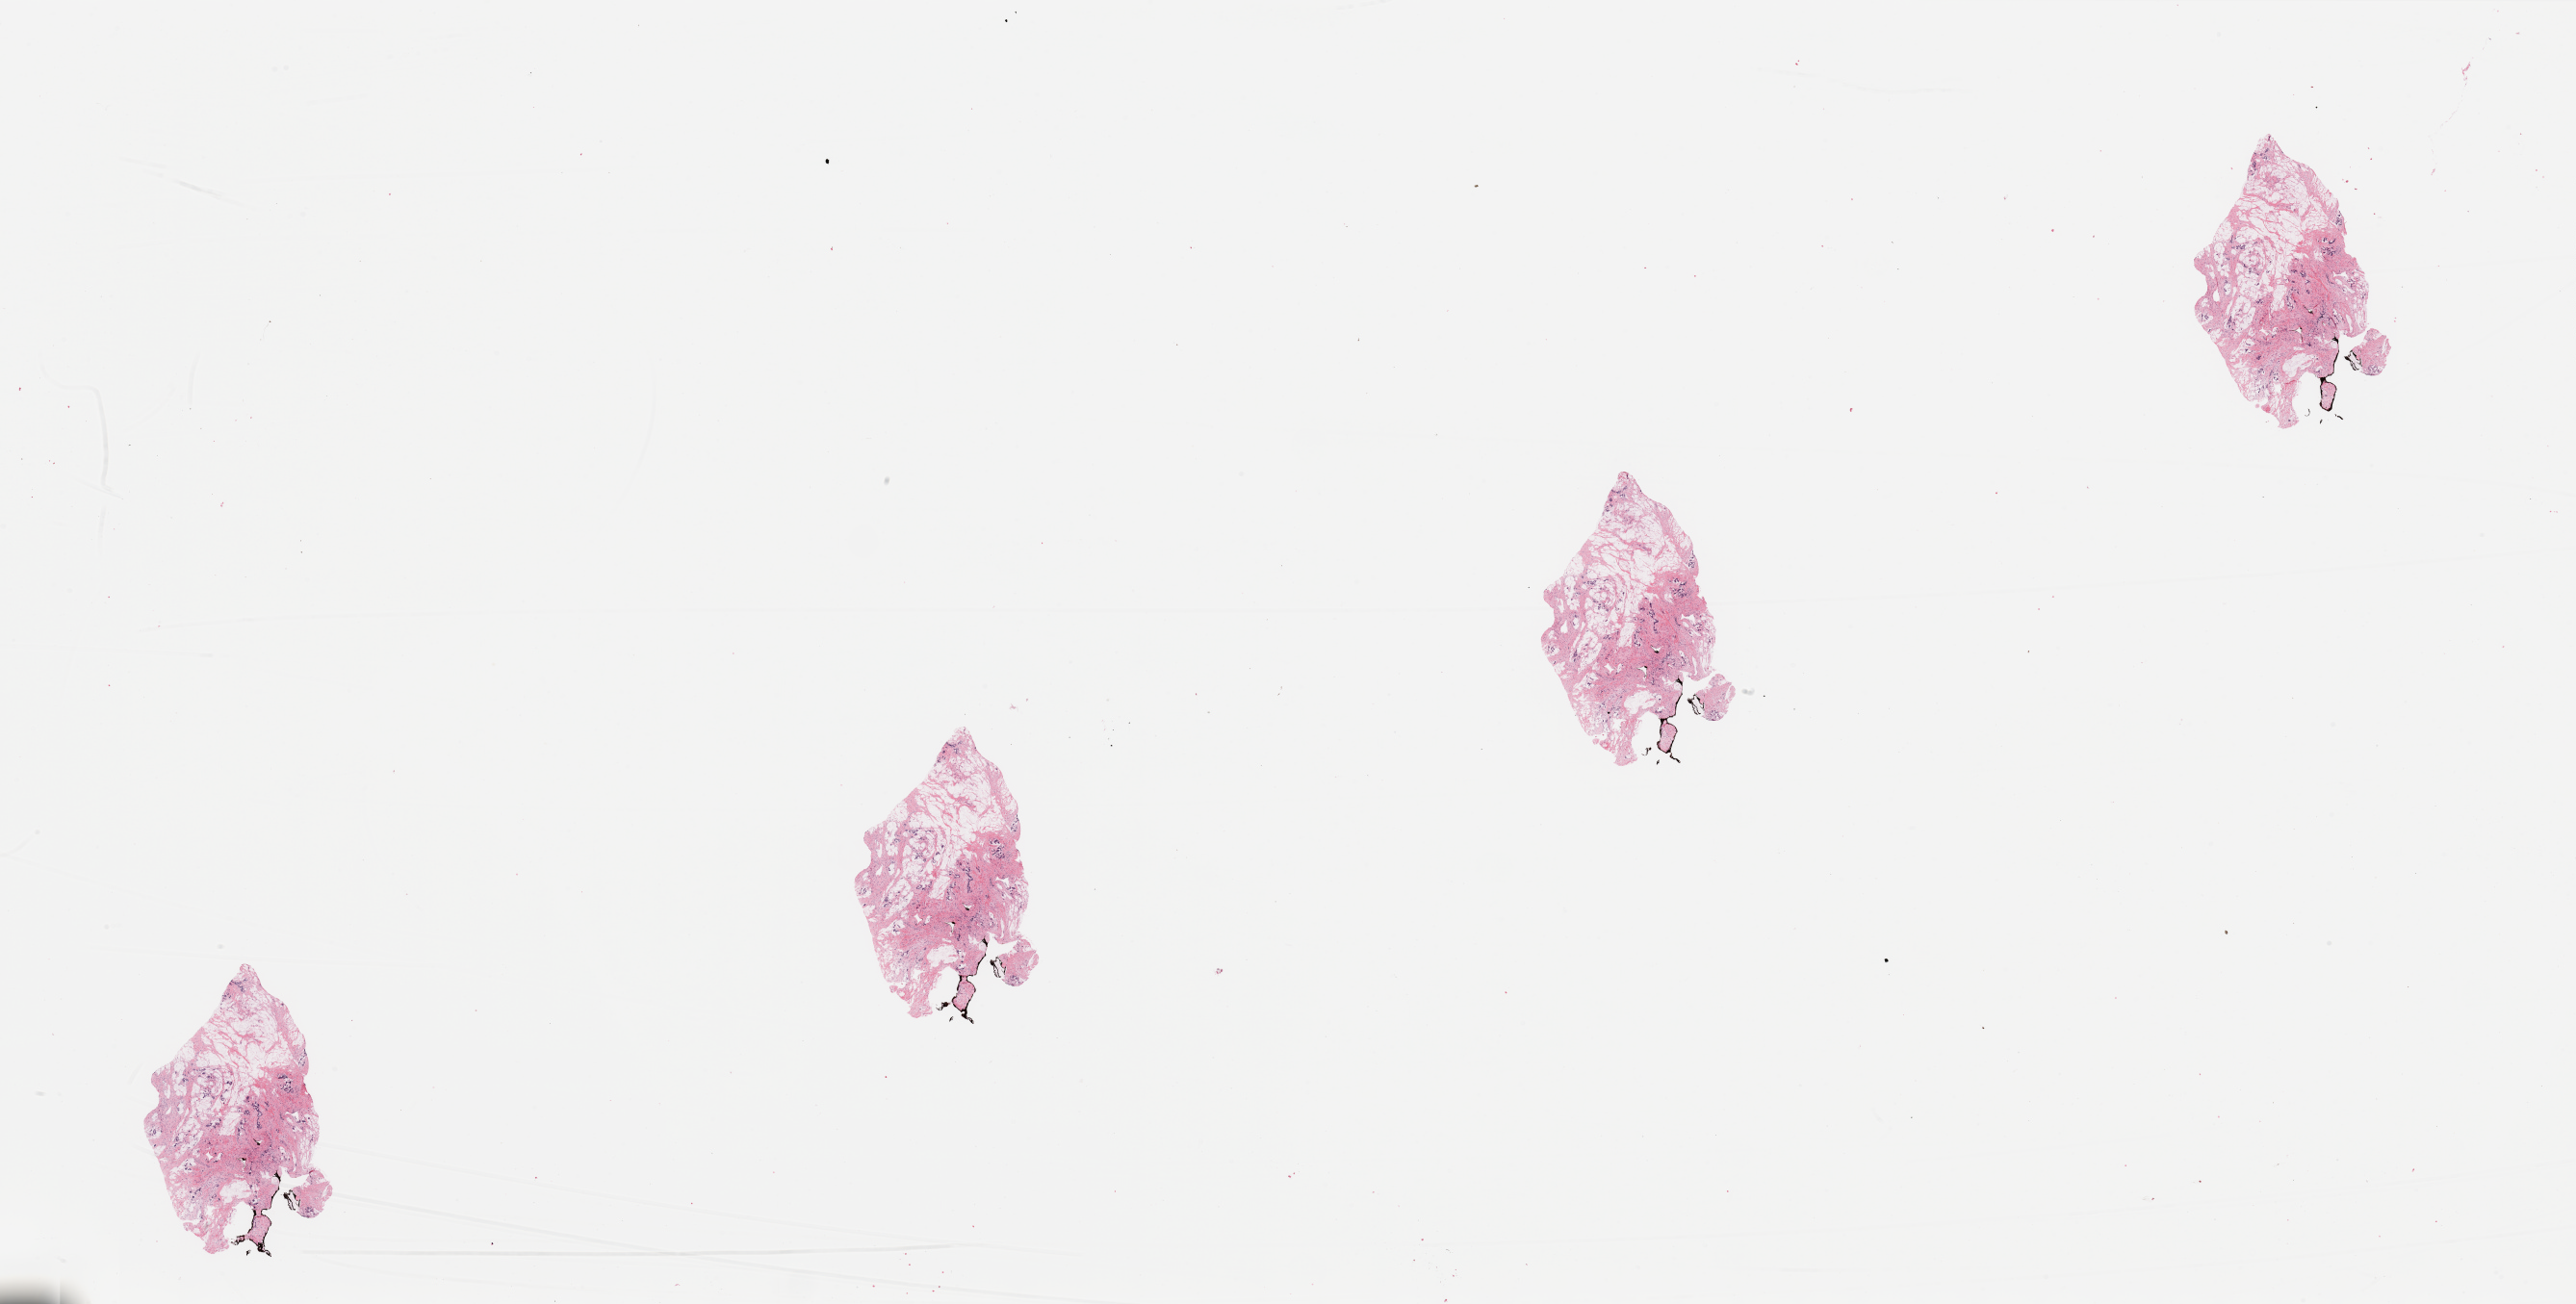
Digitized H&E-stained tissue section (whole slide), shown as a low-resolution overview of the whole scanned area (about 42.3 x 21.4 mm), tumour tissue sample, pancreas. Patient: male, age 63 years.
Patient diagnosis (cohort enrolment): ductal adenocarcinoma (pancreas).